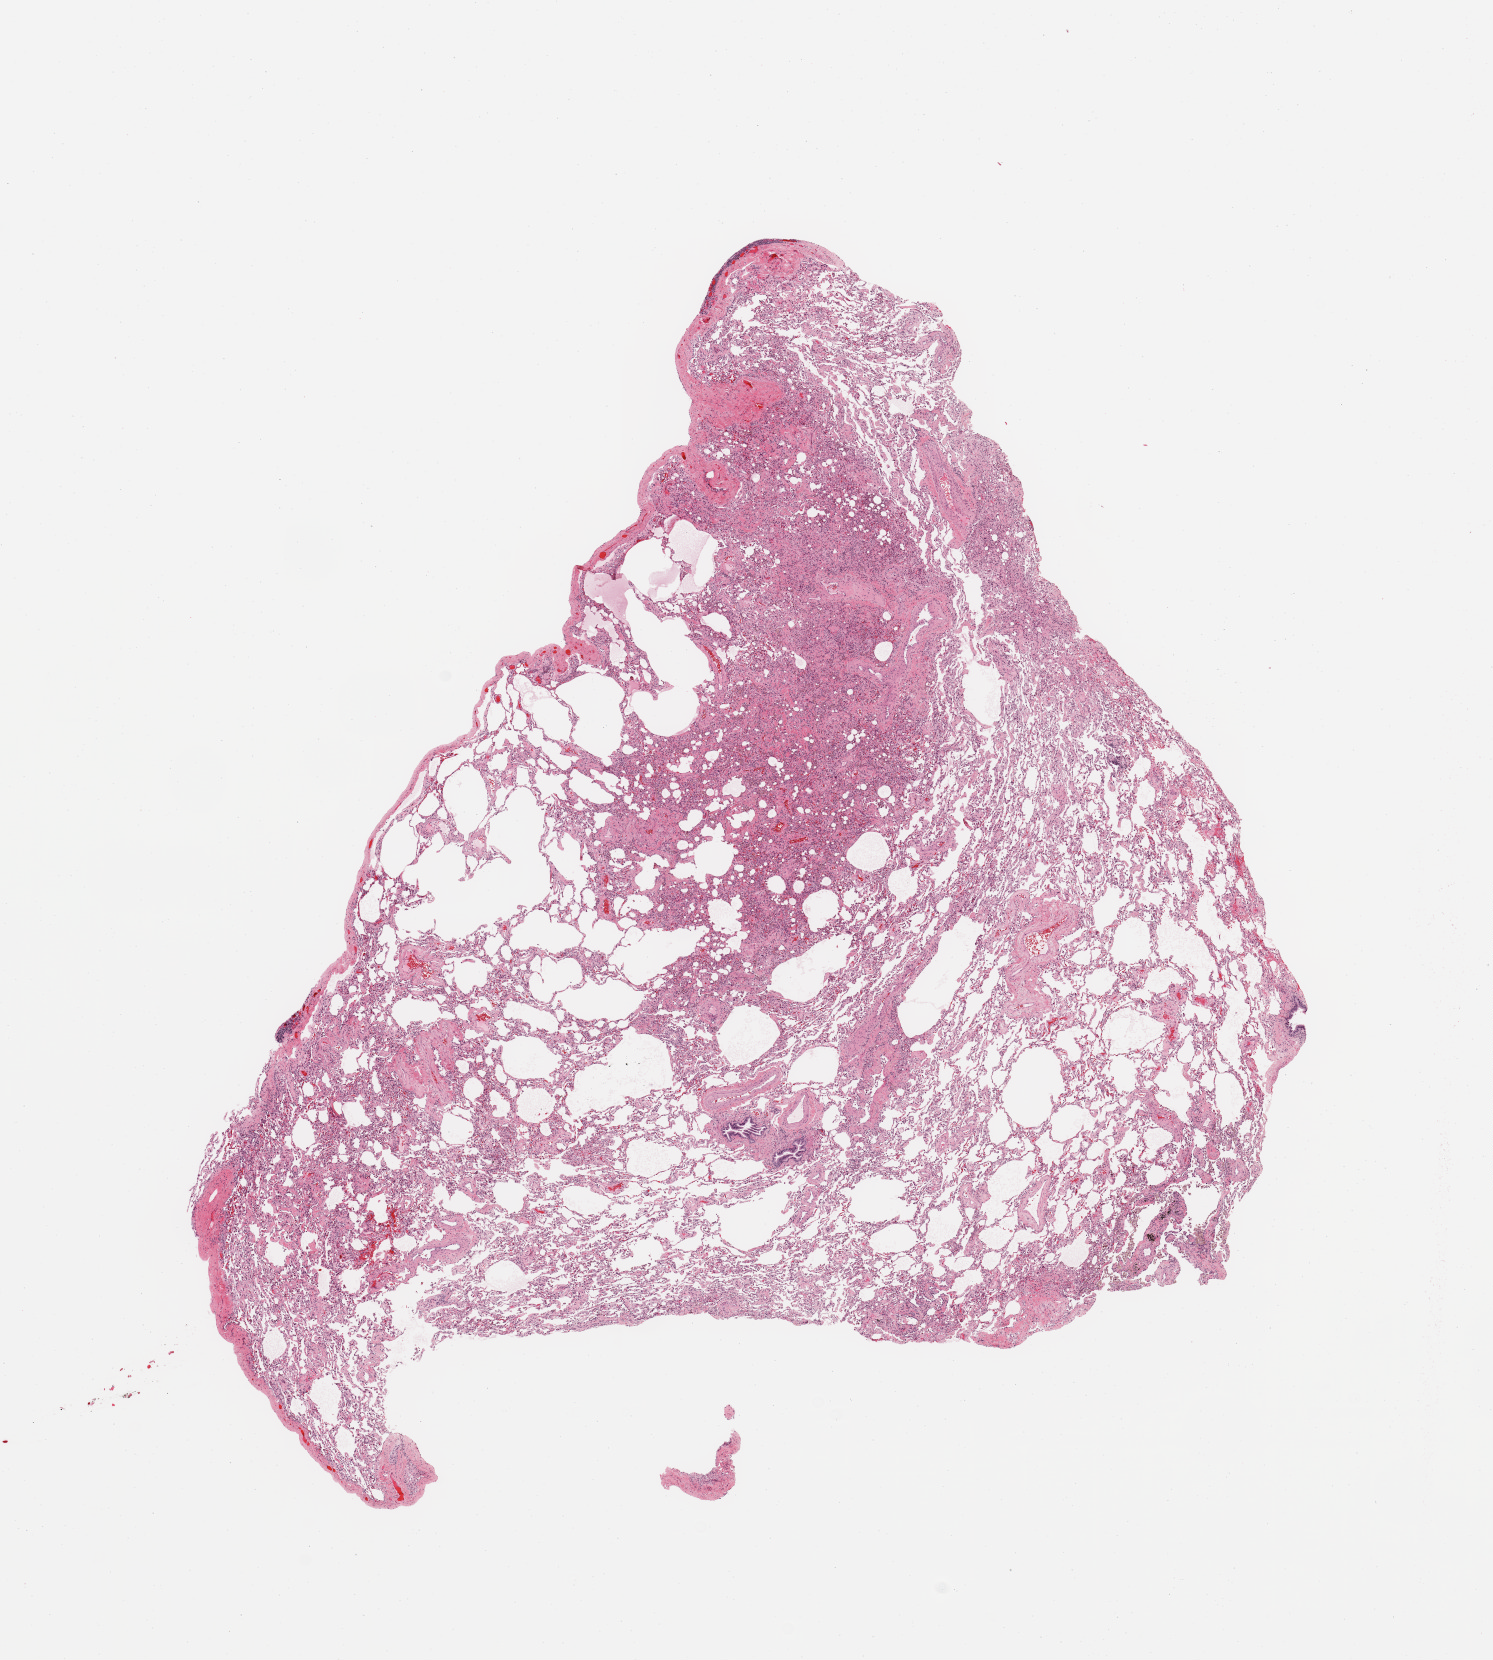
Whole-slide histology image, H&E-stained — whole scanned area (about 11.8 x 13.1 mm, slide scanned at 20x) shown as a low-resolution overview; normal (non-tumour) tissue sample, sampled site: lung. Patient: male, age 61 years.
This section: normal (non-tumour) tissue from the same patient. Patient diagnosis: Squamous cell carcinoma, NOS.